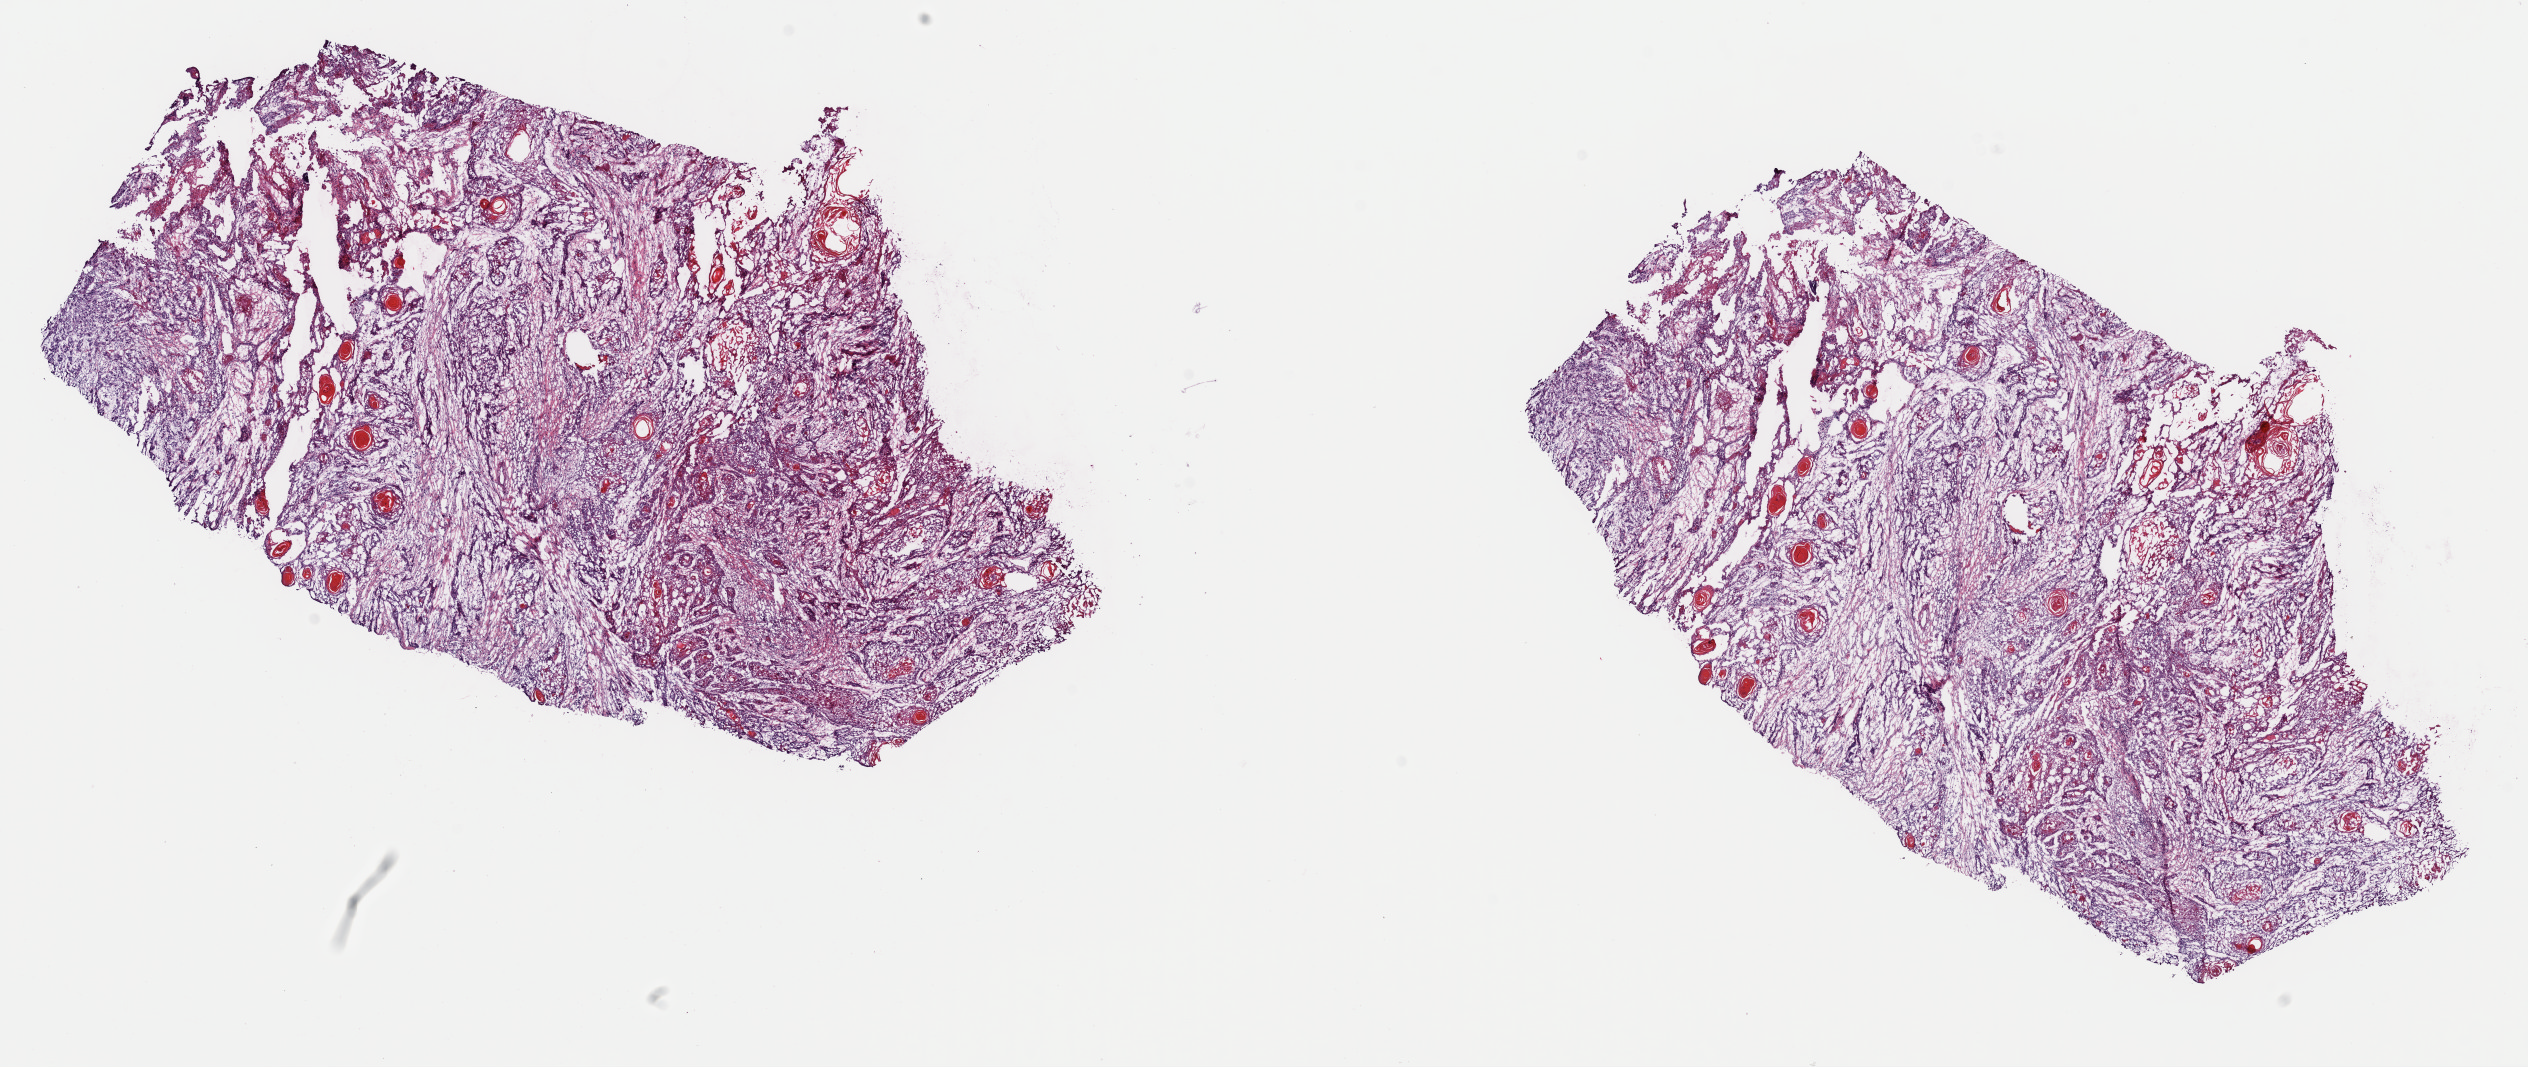
Whole-slide histology image, H&E-stained — shown as a low-resolution overview of the whole scanned area (about 20.0 x 8.4 mm, from a 40x scan), frozen section from the top of the tissue portion, primary tumour sample from the head and neck. Male, age 49 years at initial diagnosis. Histologic grade: G2 (moderately differentiated). Pathologist review of this section (percent, as recorded): tumour cells 55%, tumour nuclei 70%, normal cells 0%, stromal cells 40%, necrosis 5%. Infiltration values recorded for this section: lymphocyte infiltration 0%, monocyte infiltration 0%, neutrophil infiltration 0%.
- AJCC pathologic stage: IVA (6th edition)
- laterality: right
- pathologic diagnosis: Squamous cell carcinoma, keratinizing, NOS (mouth, NOS)